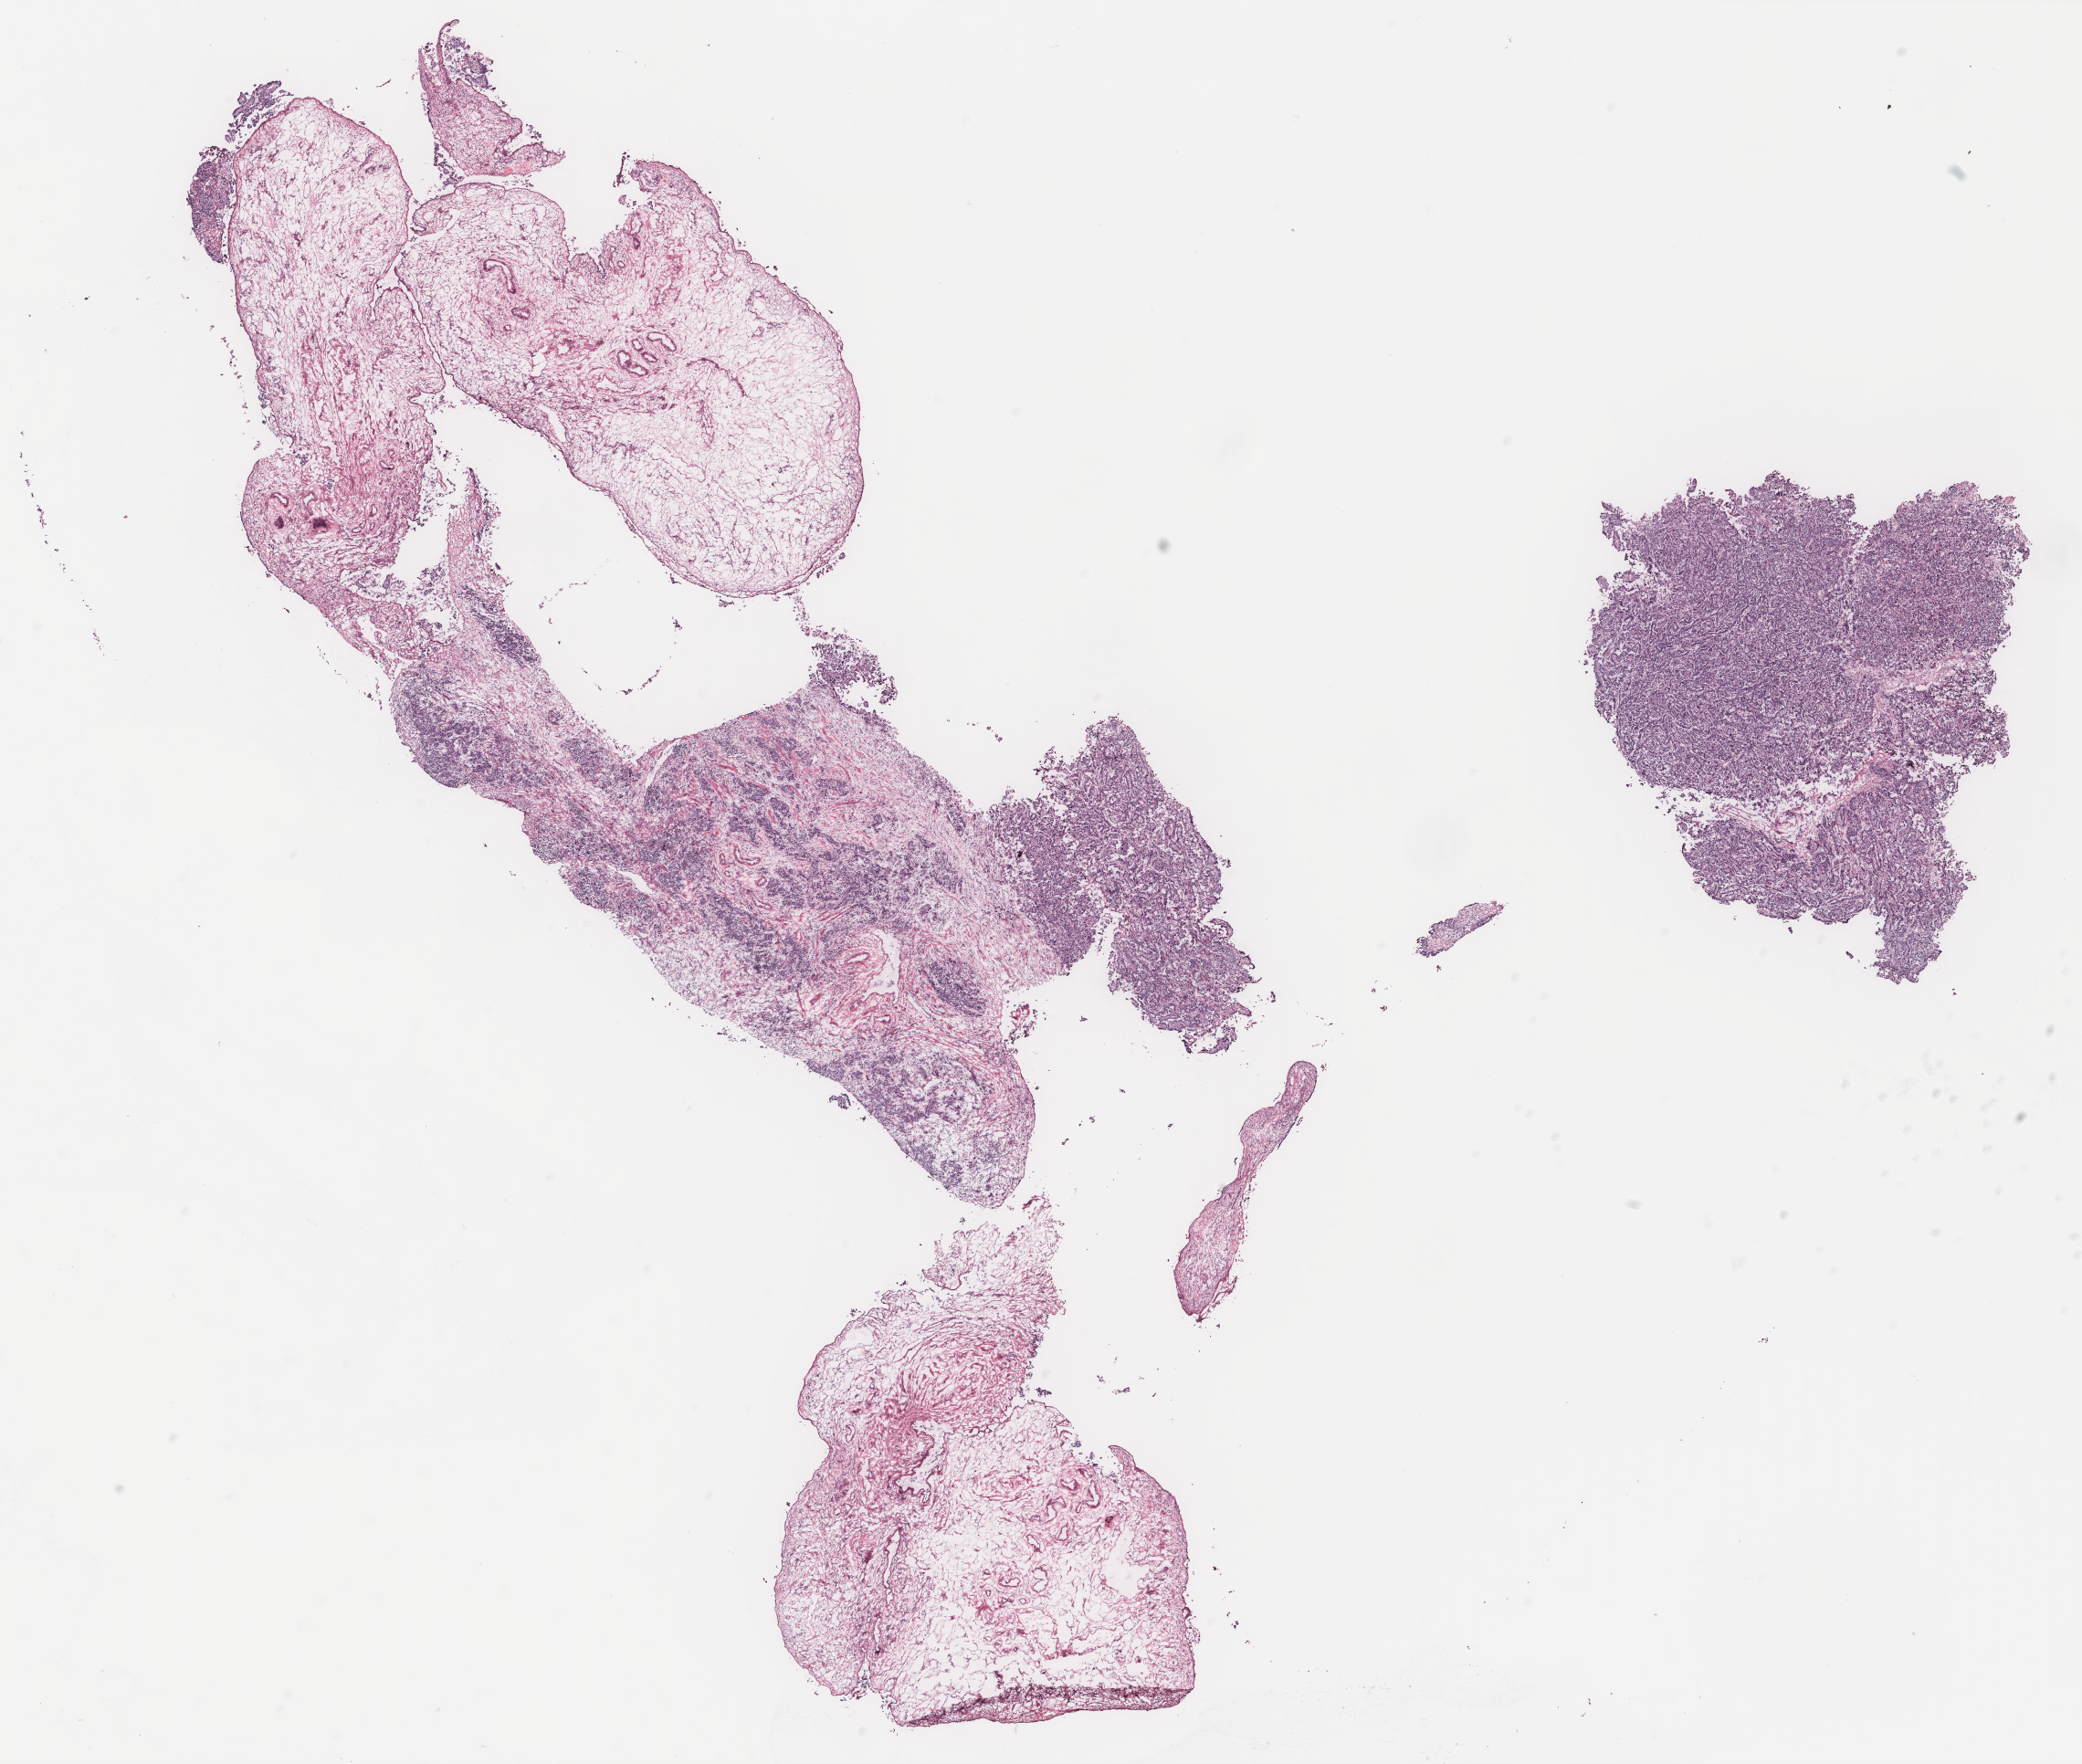
Digitized H&E-stained tissue section (whole slide) — low-resolution overview of the scanned area, about 18.2 x 15.5 mm (slide scanned at 40x); ovary, tissue type not recorded. Patient sex: female.
Patient diagnosis: Serous adenocarcinoma, NOS.